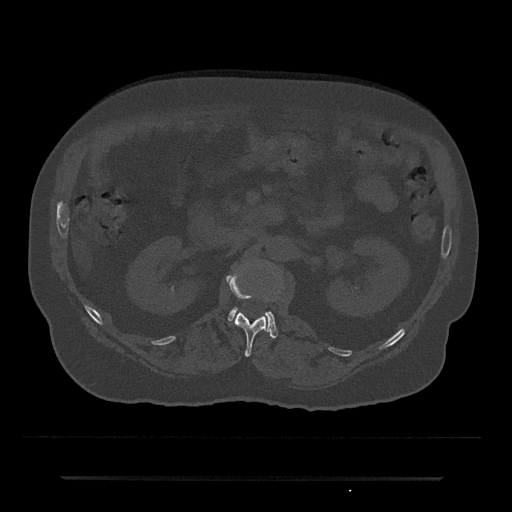
CT including the spine, one axial slice. Position 48 of 797 along the scan axis. Bone window (W 1800 / L 400 HU). 0.5 mm slice thickness. 512 × 512 image matrix, field of view 437 × 437 mm. Patient: male, 69 years. From the clinical record (not read from this slice): primary cancer: prostate.
Outlined on this slice (semi-automatically segmented with operator editing):
- L1 vertebra: bounding box <226,266,266,357> (left, top, right, bottom; pixels)
- L2 vertebra: <228,308,278,338>